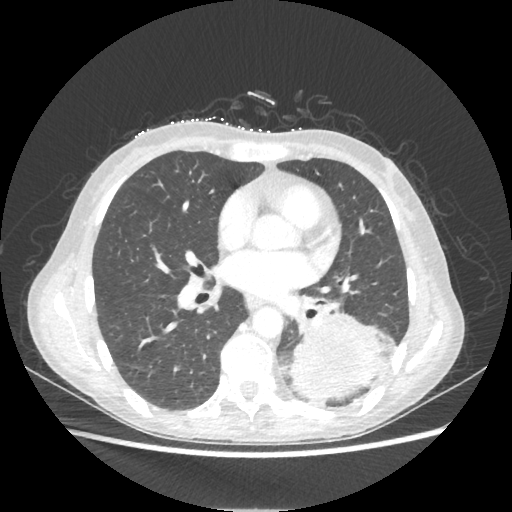
Chest CT, one axial slice; slice 105 of 221 in the series (ordered by position); lung window (W 1500 / L -600 HU); 512 × 512 image matrix, field of view 360 × 360 mm. Patient: female, 53 years. Case-level facts recorded for this patient, not image findings: clinical TNM (as recorded): T3 N0 M0.
Structures marked on this image (bounding box drawn by a radiologist):
- lung tumour (recorded histology: adenocarcinoma): bounding box <290,314,382,400> (left, top, right, bottom; pixels)